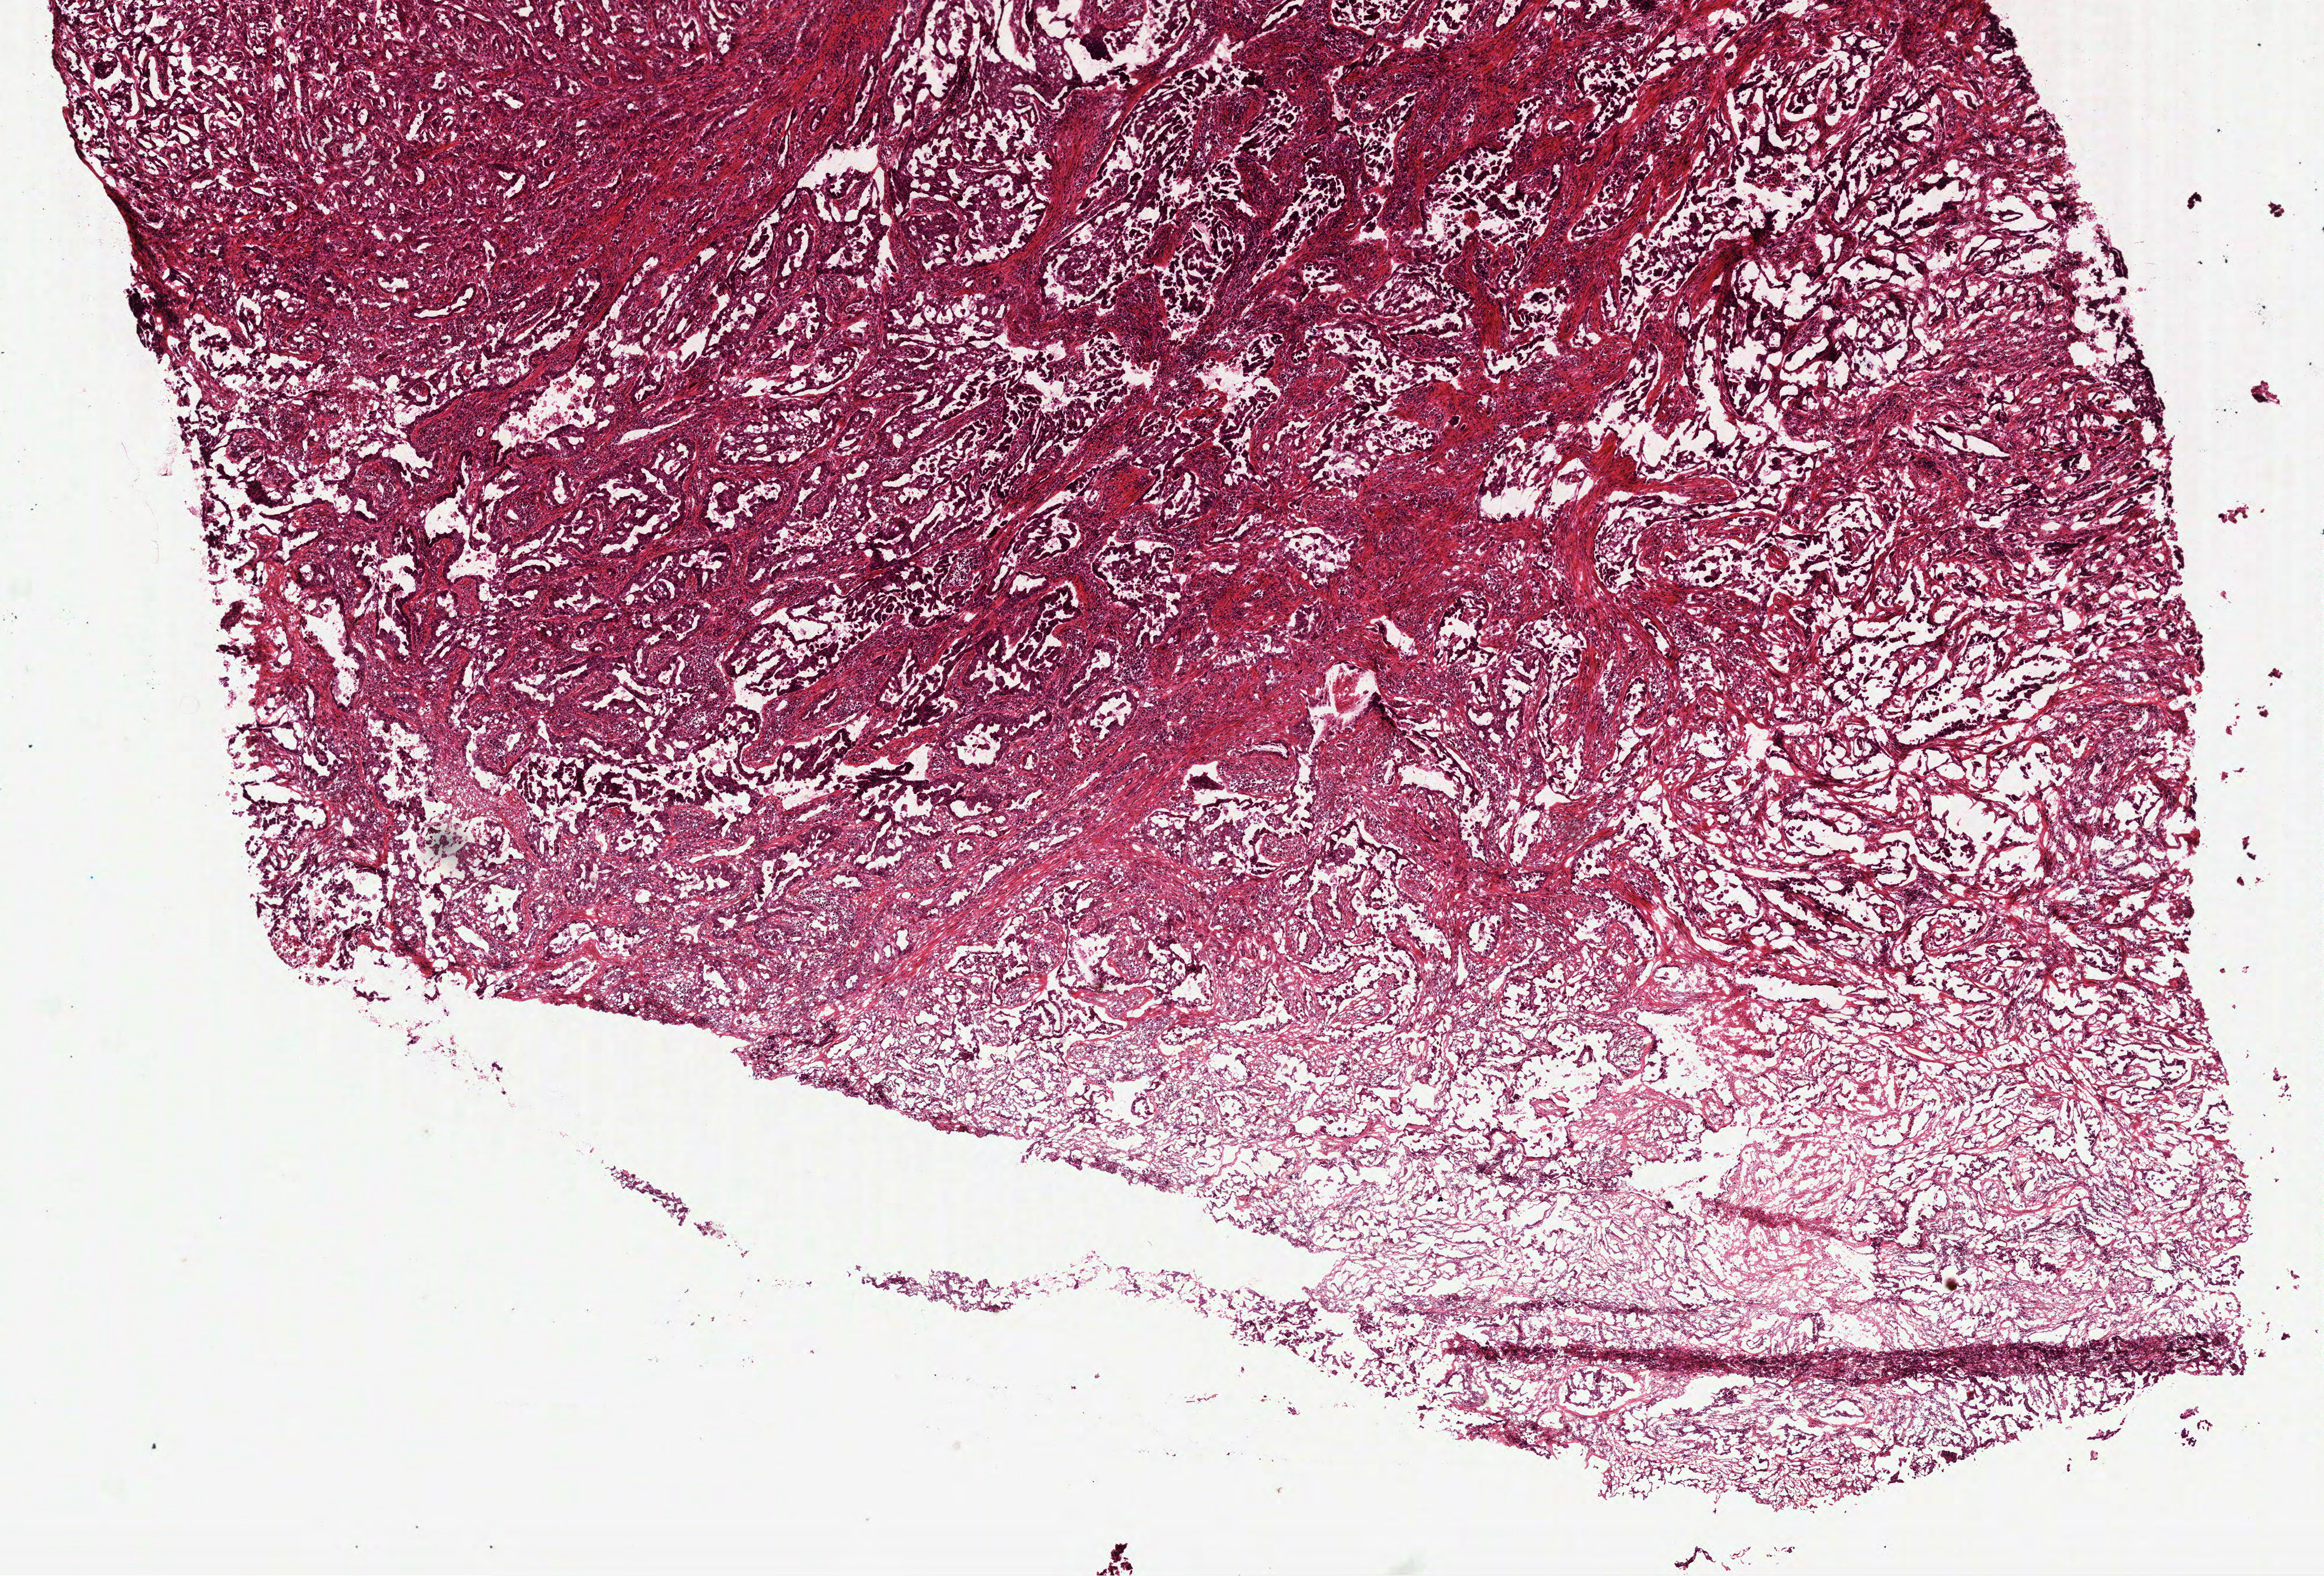
Digitized H&E tissue section (whole slide), shown as a low-resolution overview of the whole scanned area (about 8.0 x 5.4 mm, from a 40x scan), frozen section from the top of the tissue portion, primary tumour sample from the lung. Male patient; age at initial diagnosis 61 years.
Histologic diagnosis: Adenocarcinoma with mixed subtypes (upper lobe, lung).